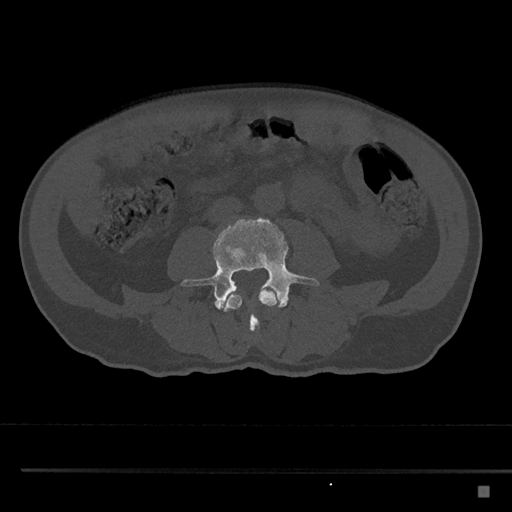
CT including the spine, one axial slice; position 655 of 797 along the scan axis; reconstruction kernel Br40s/3; 120 kVp; bone window (W 1800 / L 400 HU); 0.5 mm slice thickness; 512 × 512 image matrix. Male patient, age 59 years. Case-level facts recorded for this patient, not image findings: primary cancer: prostate.
Structures marked on this image (semi-automatic segmentation, software-assisted and operator-edited):
- L3 vertebra: box from (x=219, y=287) to (x=278, y=332) px
- L4 vertebra: (x=181, y=218)–(x=319, y=309)